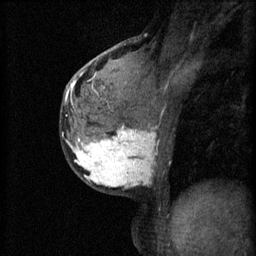
Breast MRI (dynamic contrast-enhanced), one sagittal slice; slice 32 of 60 in the series (ordered by position); 3 images stored at this slice position (order not interpretable as contrast timing); 1.5 T; TE 4.2 ms, TR 11 ms; 2 mm slice thickness; 256 × 256 image matrix. Female patient, age 37 years.
Outlined on this slice (semi-automatic segmentation, software-assisted and operator-edited):
- analysis volume of interest (the breast-tissue region the enhancement analysis was run in; not a lesion): box from (x=68, y=118) to (x=164, y=193) px
- tumour enhancement mask (voxels above the 70 % enhancement threshold inside the analysis volume of interest): (x=68, y=126)–(x=156, y=189)